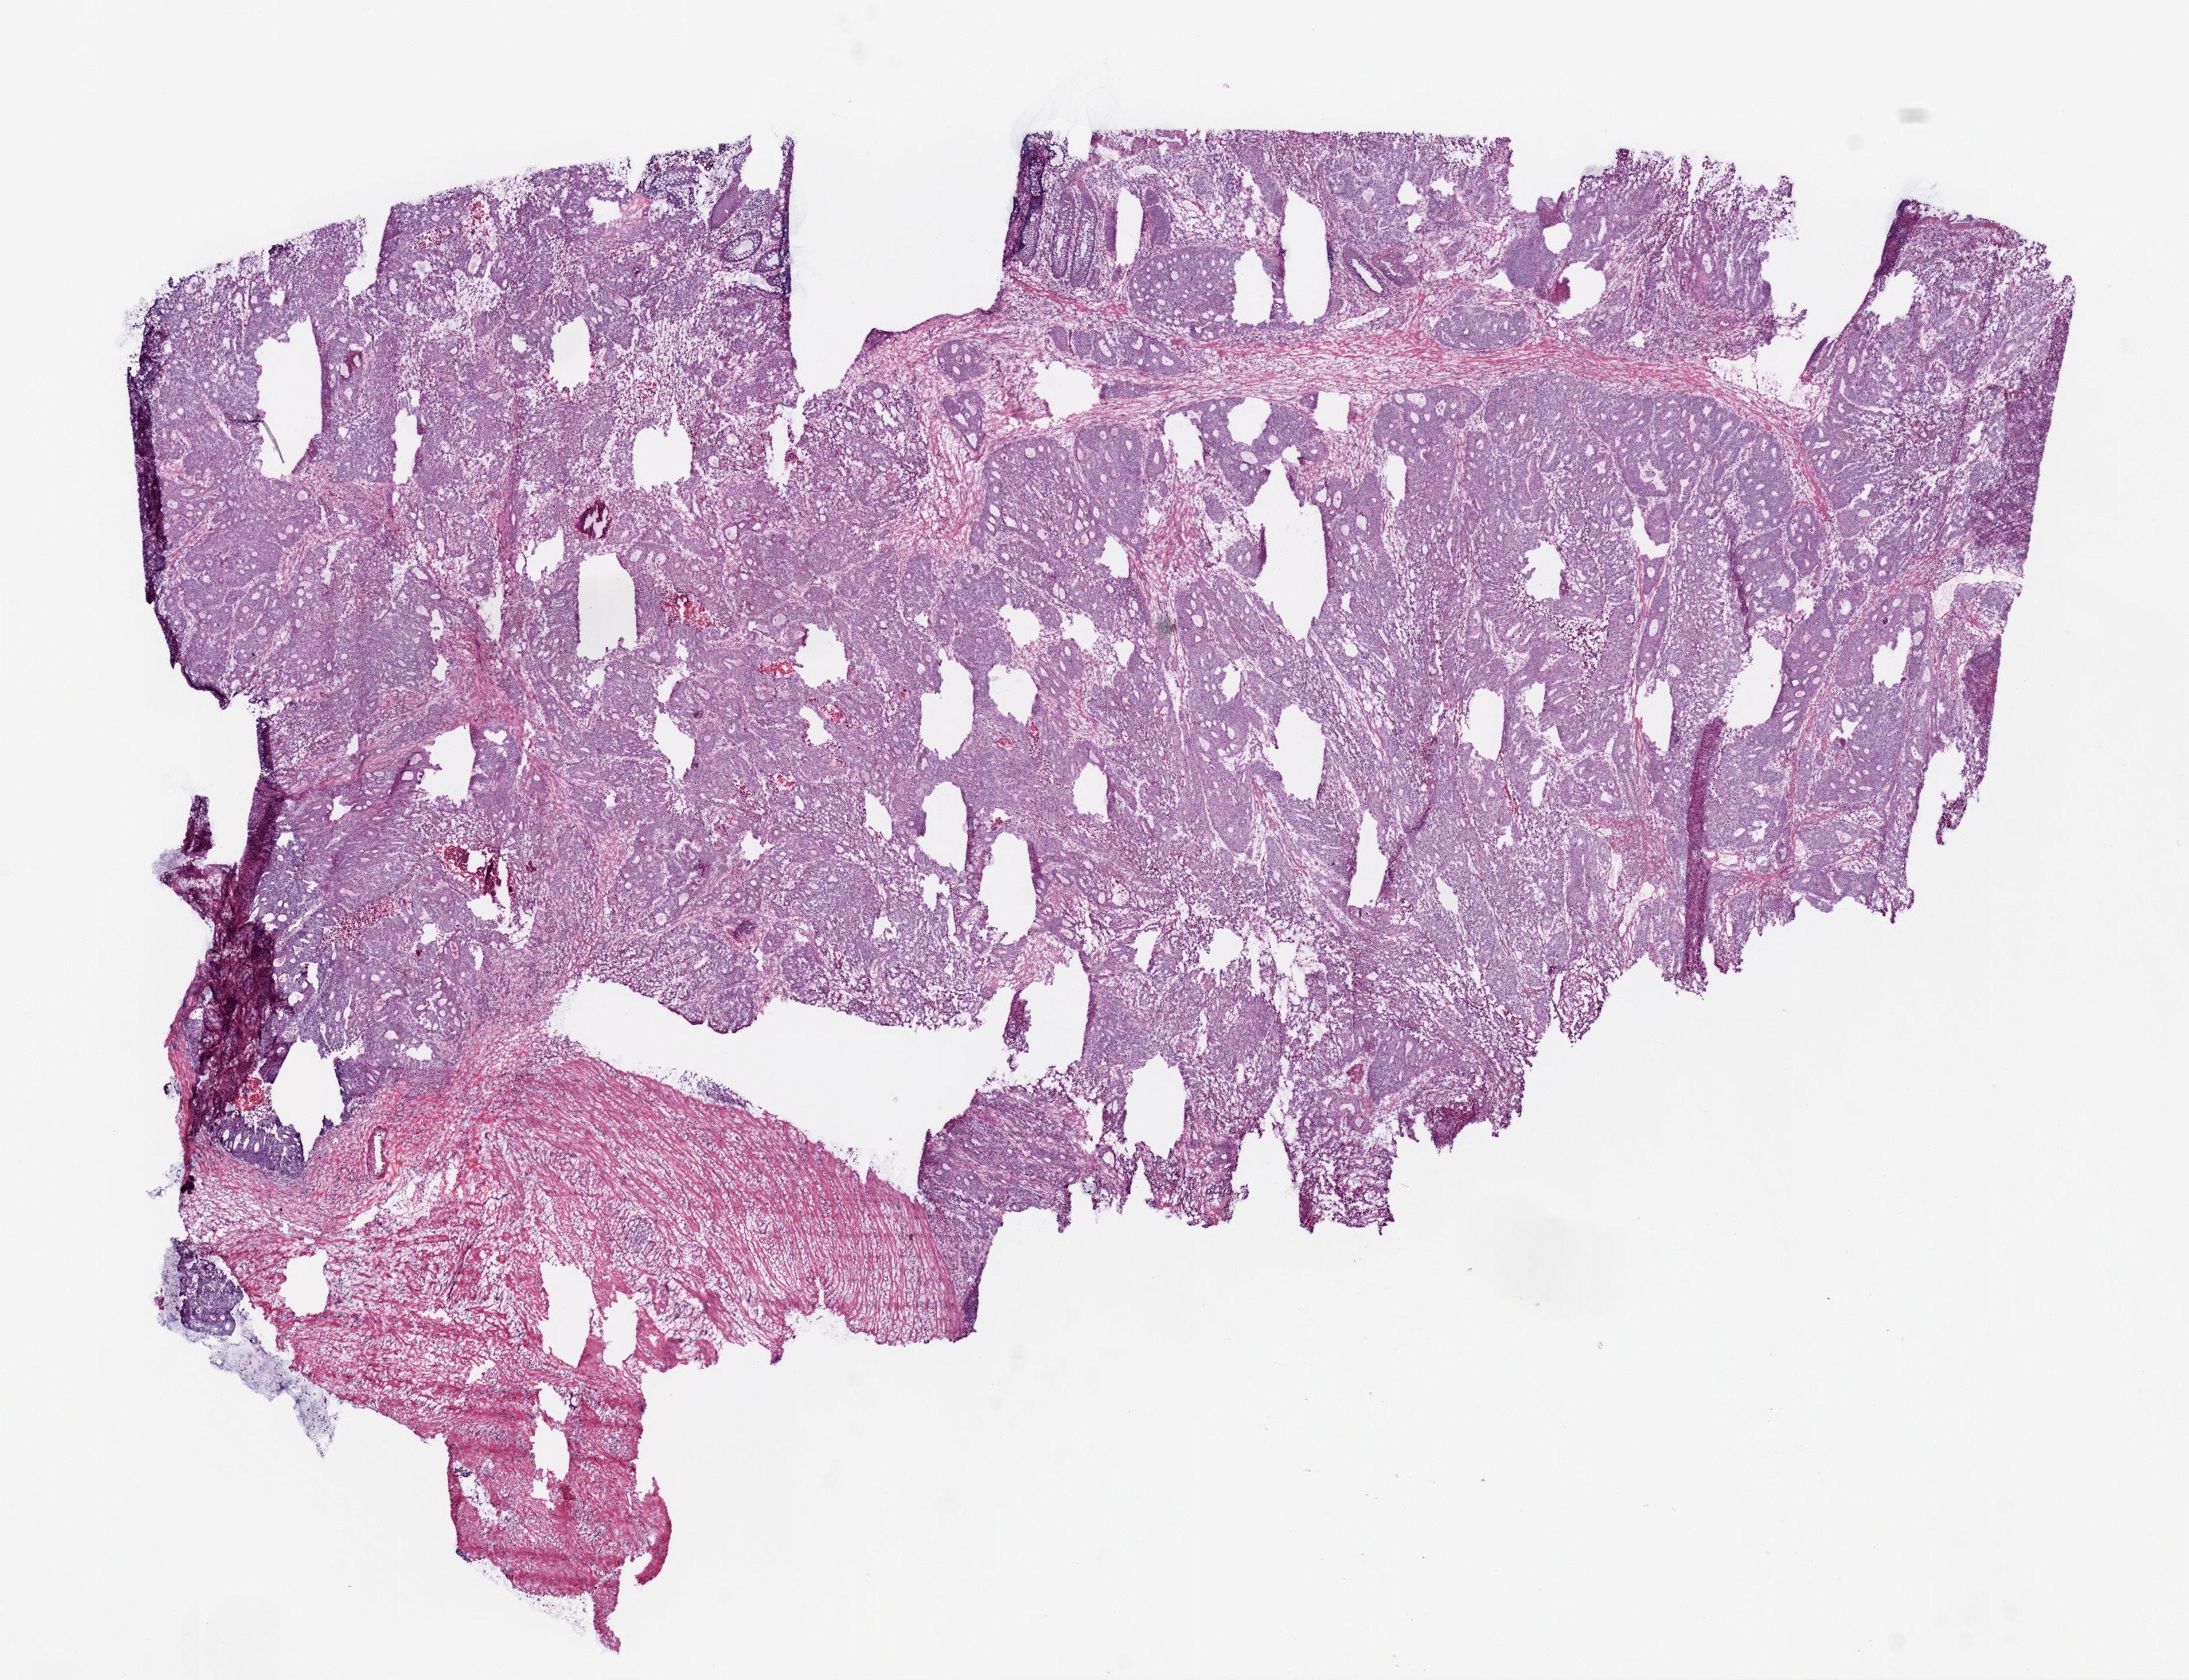
Digitized H&E tissue section (whole slide), shown as a low-resolution overview of the whole scanned area (about 11.0 x 8.5 mm), frozen section, sample: primary tumour, rectum. Patient: male, age at initial diagnosis 60 years. Slide review estimates, as recorded: tumour cells 72%, tumour nuclei 75%, normal cells 15%, stromal cells 5%, necrosis 8%.
AJCC pathologic stage: IV. Histologic diagnosis: Adenocarcinoma, NOS. TNM: T3 N2 M1. Lymph nodes positive (case pathology): 20 of 34 examined.